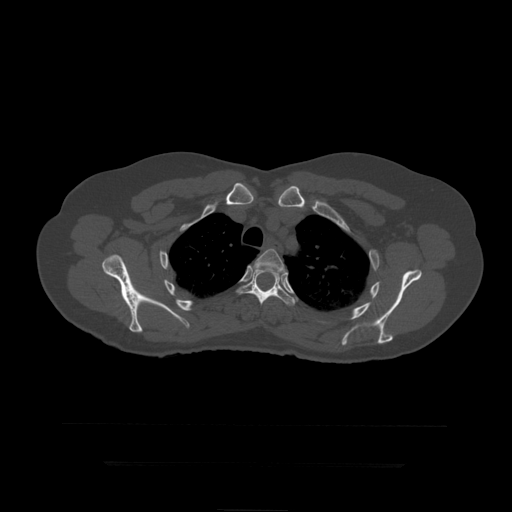
CT including the spine, one axial slice; position 340 of 399 along the scan axis; reconstruction kernel STANDARD; 120 kVp; bone window (W 1800 / L 400 HU); 512 × 512 image matrix. Patient age 41 years. Case-level facts recorded for this patient, not image findings: primary cancer: breast.
Structures marked on this image (semi-automatic segmentation, software-assisted and operator-edited):
- T4 vertebra: bounding box (x1, y1, x2, y2) in pixels: (253, 249, 285, 276)
- T5 vertebra: (236, 269, 296, 306)